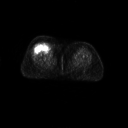
FDG PET of an extremity soft-tissue mass (from a PET/CT study), one axial slice; slice 26 of 267 in the series (ordered by position); 3.27 mm slice thickness; 128 × 128 image matrix, field of view 700 × 700 mm. Female patient, age 56 years. Case-level facts recorded for this patient, not image findings: histological type: malignant solitary fibrous tumor; grade: intermediate; site of the primary tumour: right thigh.
Annotated regions visible in this slice (expert contour drawn on MRI and transferred to this co-registered scan by the dataset authors):
- gross tumour volume including surrounding oedema: bounding box [x1, y1, x2, y2] px = [36, 41, 54, 55]
- gross tumour volume (mass): [37, 42, 52, 54]